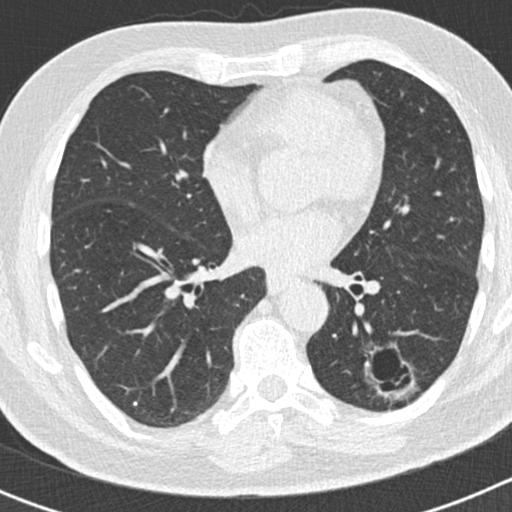
Low-dose screening chest CT, axial slice, second screening round (one year after baseline), lung window (W 1500 / L -600 HU), 2 mm slice thickness, standard (soft-tissue) reconstruction kernel (B30f), slice 92 of 186 in the series, 512 × 512 image matrix. Male, age 66 years at enrolment. Former smoker at enrolment.
• Expert-annotated lung lesion, box from (x=350, y=334) to (x=414, y=406) px.
• Screening reader's record for this exam (one nodule recorded; not confirmed to be the boxed lesion): non-calcified nodule or mass ≥4 mm, left lower lobe, 50 × 33 mm, smooth margins, pre-existing on the prior screen: yes; interval growth: yes.
• Later outcome: lung cancer diagnosed 440 days after this screen — adenocarcinoma, NOS, left lower lobe, poorly differentiated (G3), stage IB (AJCC 6th edition), 38 mm at pathology.